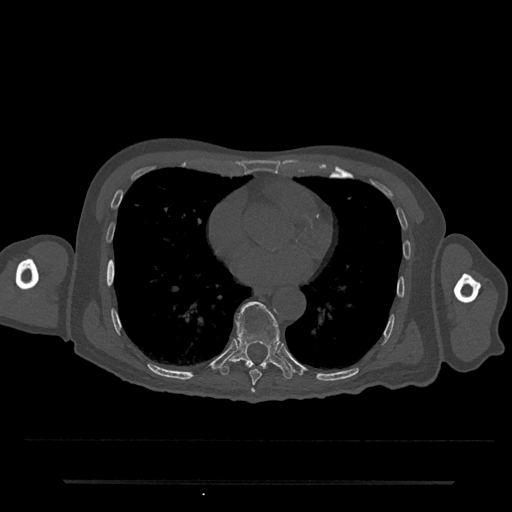
CT including the spine, one axial slice; position 389 of 797 along the scan axis; reconstruction kernel Br40s/3; 120 kVp; bone window (W 1800 / L 400 HU); 0.5 mm slice thickness; 512 × 512 image matrix. Patient: male, 74 years. Case-level facts recorded for this patient, not image findings: primary cancer: prostate.
Structures marked on this image (semi-automatic segmentation, software-assisted and operator-edited):
- T7 vertebra: box from (x=251, y=388) to (x=255, y=393) px
- T8 vertebra: (x=249, y=370)–(x=262, y=385)
- T9 vertebra: (x=221, y=301)–(x=293, y=379)